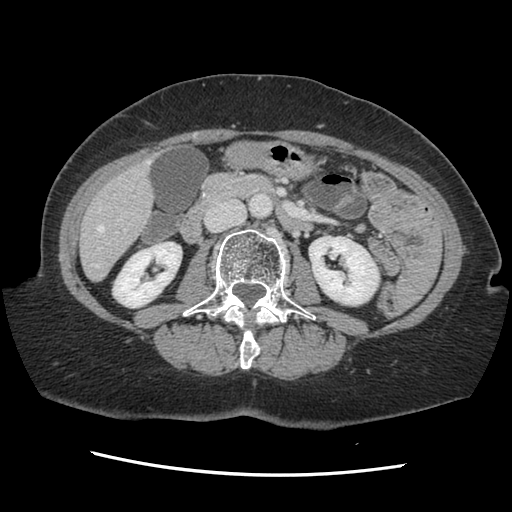
Contrast-enhanced abdominal CT, one axial slice. Slice 47 of 141 in the series (ordered by position). Soft-tissue window (W 400 / L 40 HU). 512 × 512 image matrix, field of view 330 × 330 mm. Female patient, age 61 years. From the clinical record (not read from this slice): diagnosis: colorectal cancer liver metastases, imaged before liver resection; multiple liver metastases: no; largest metastasis: 2.4 cm; disease in both lobes: no.
Structures marked on this image (manually delineated by an expert):
- hepatic veins: bounding box [x1, y1, x2, y2] px = [93, 162, 148, 267]
- liver: [82, 163, 153, 280]
- planned liver remnant (the part of the liver to remain after resection): [82, 186, 153, 280]
- portal vein (with intrahepatic branches): [98, 229, 126, 250]